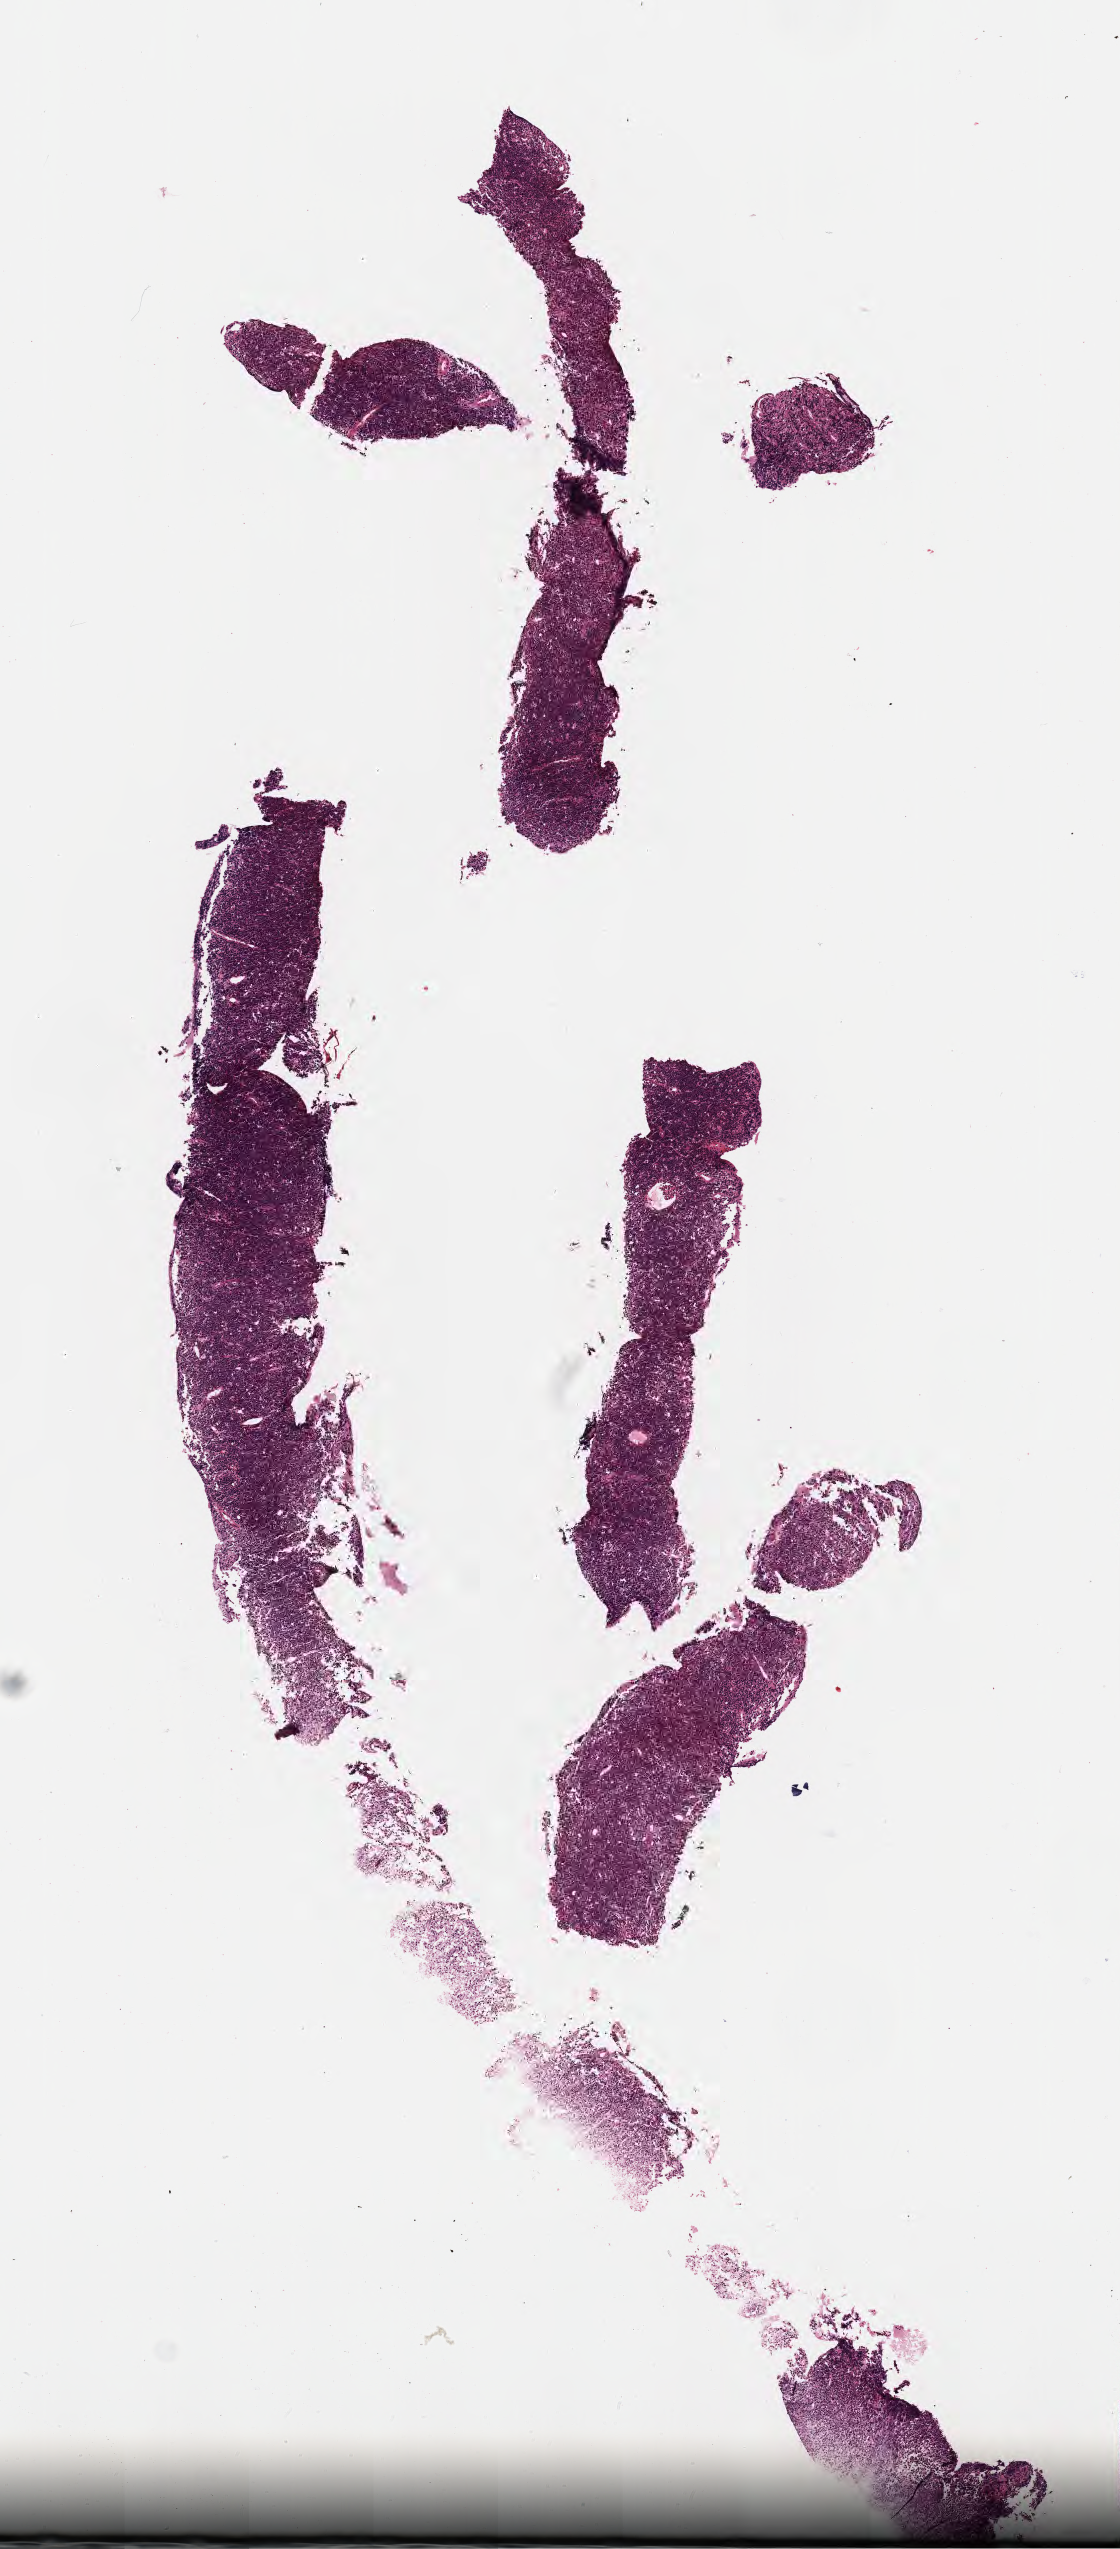
Whole-slide image, H&E stain, low-resolution overview of the scanned area, about 4.5 x 10.3 mm. FFPE section. Primary tumor. Male, age 8 years at initial diagnosis. Slide review estimates, as recorded: tumor cells 90%, tumor nuclei 90%, stromal cells 5%, necrosis 5%, normal cells 0%. Inflammatory infiltration, as recorded: lymphocyte infiltration 20%, monocyte infiltration 30%, neutrophil infiltration 5%.
• Ann Arbor stage (patient): Stage III
• histologic diagnosis: Burkitt lymphoma, NOS